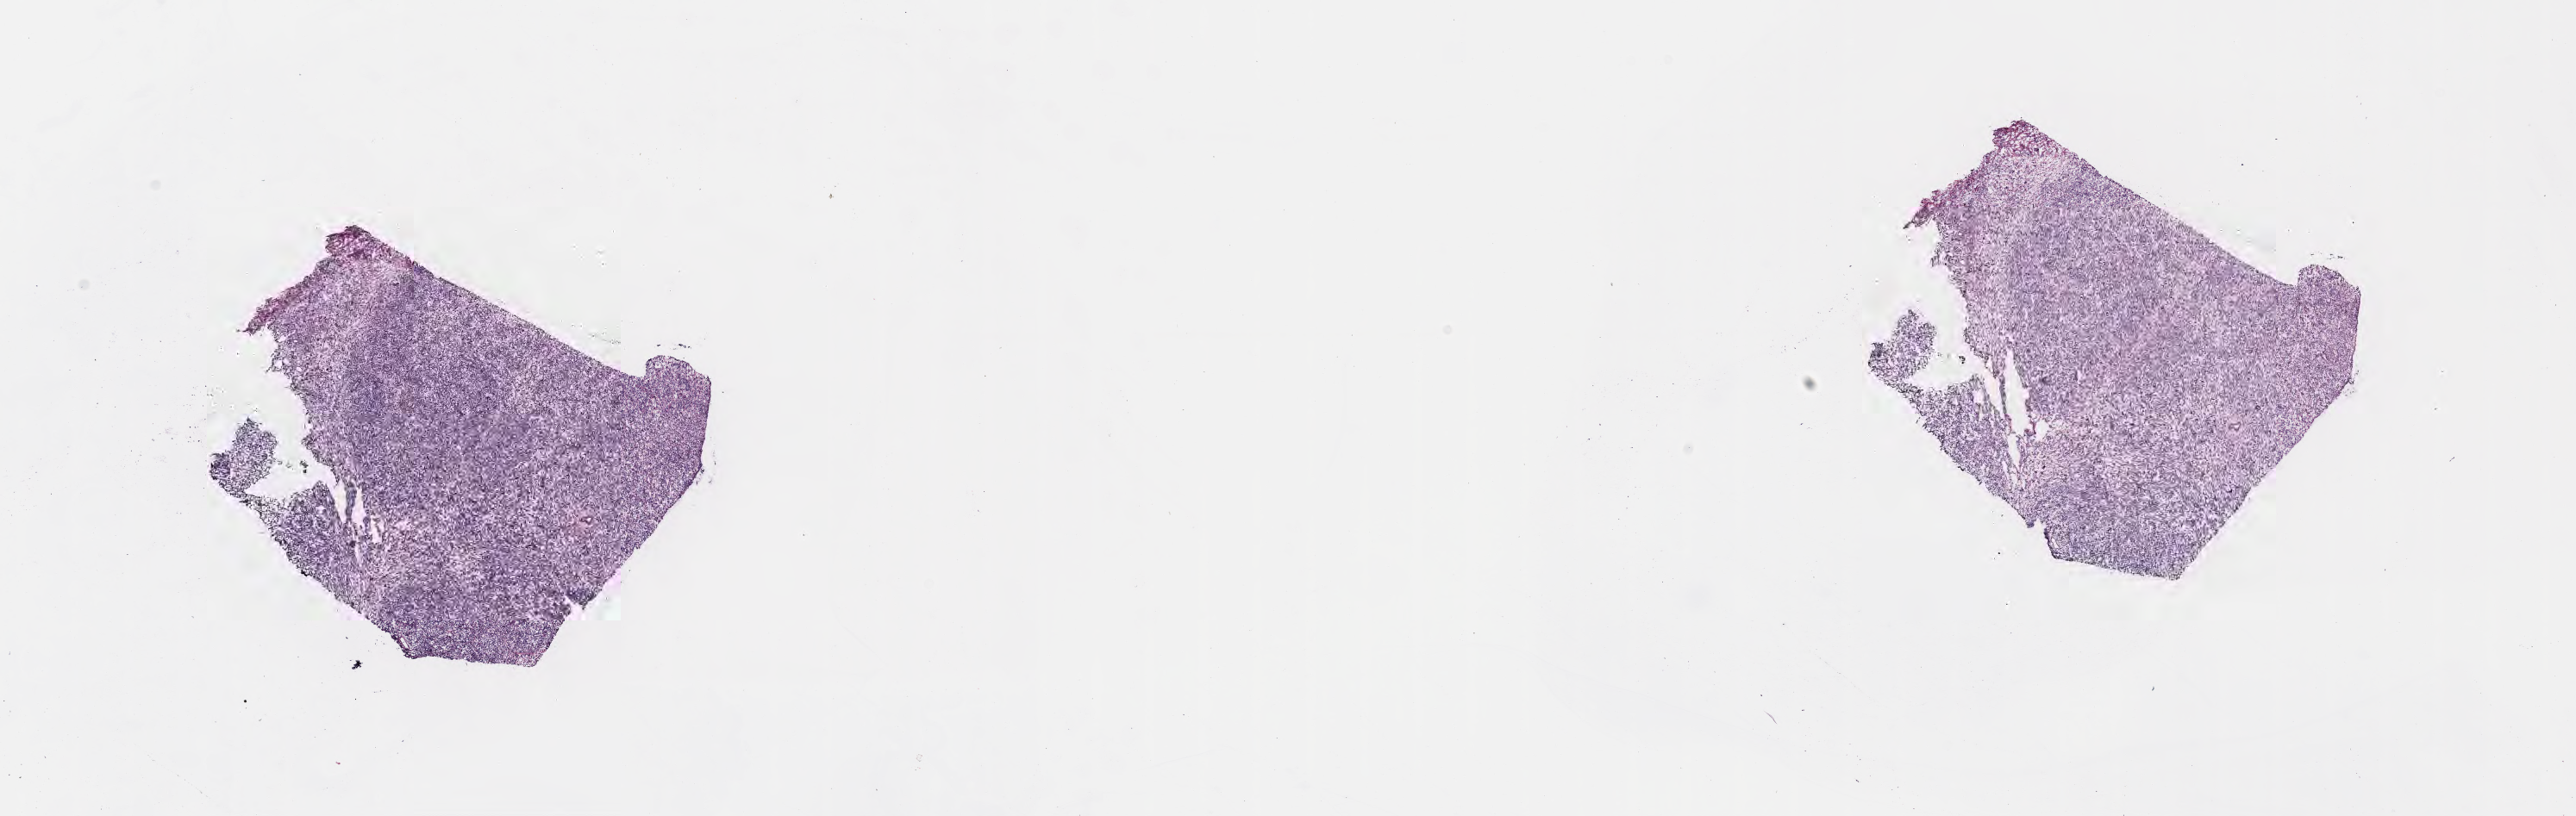
Whole-slide image, haematoxylin and eosin stain, a low-resolution overview of the entire scanned area, about 24.1 x 7.7 mm, frozen section (tissue freezing medium), recurrent tumor, site: testis. Male, age 8 years at initial diagnosis. Slide review estimates, as recorded: tumor cells 85%, tumor nuclei 90%, stromal cells 10%, necrosis 5%, normal cells 0%. Infiltration values recorded for this section: lymphocyte infiltration 50%, monocyte infiltration 20%, neutrophil infiltration 0%.
Section: bottom of the tissue portion. Patient diagnosis: Burkitt lymphoma, NOS.